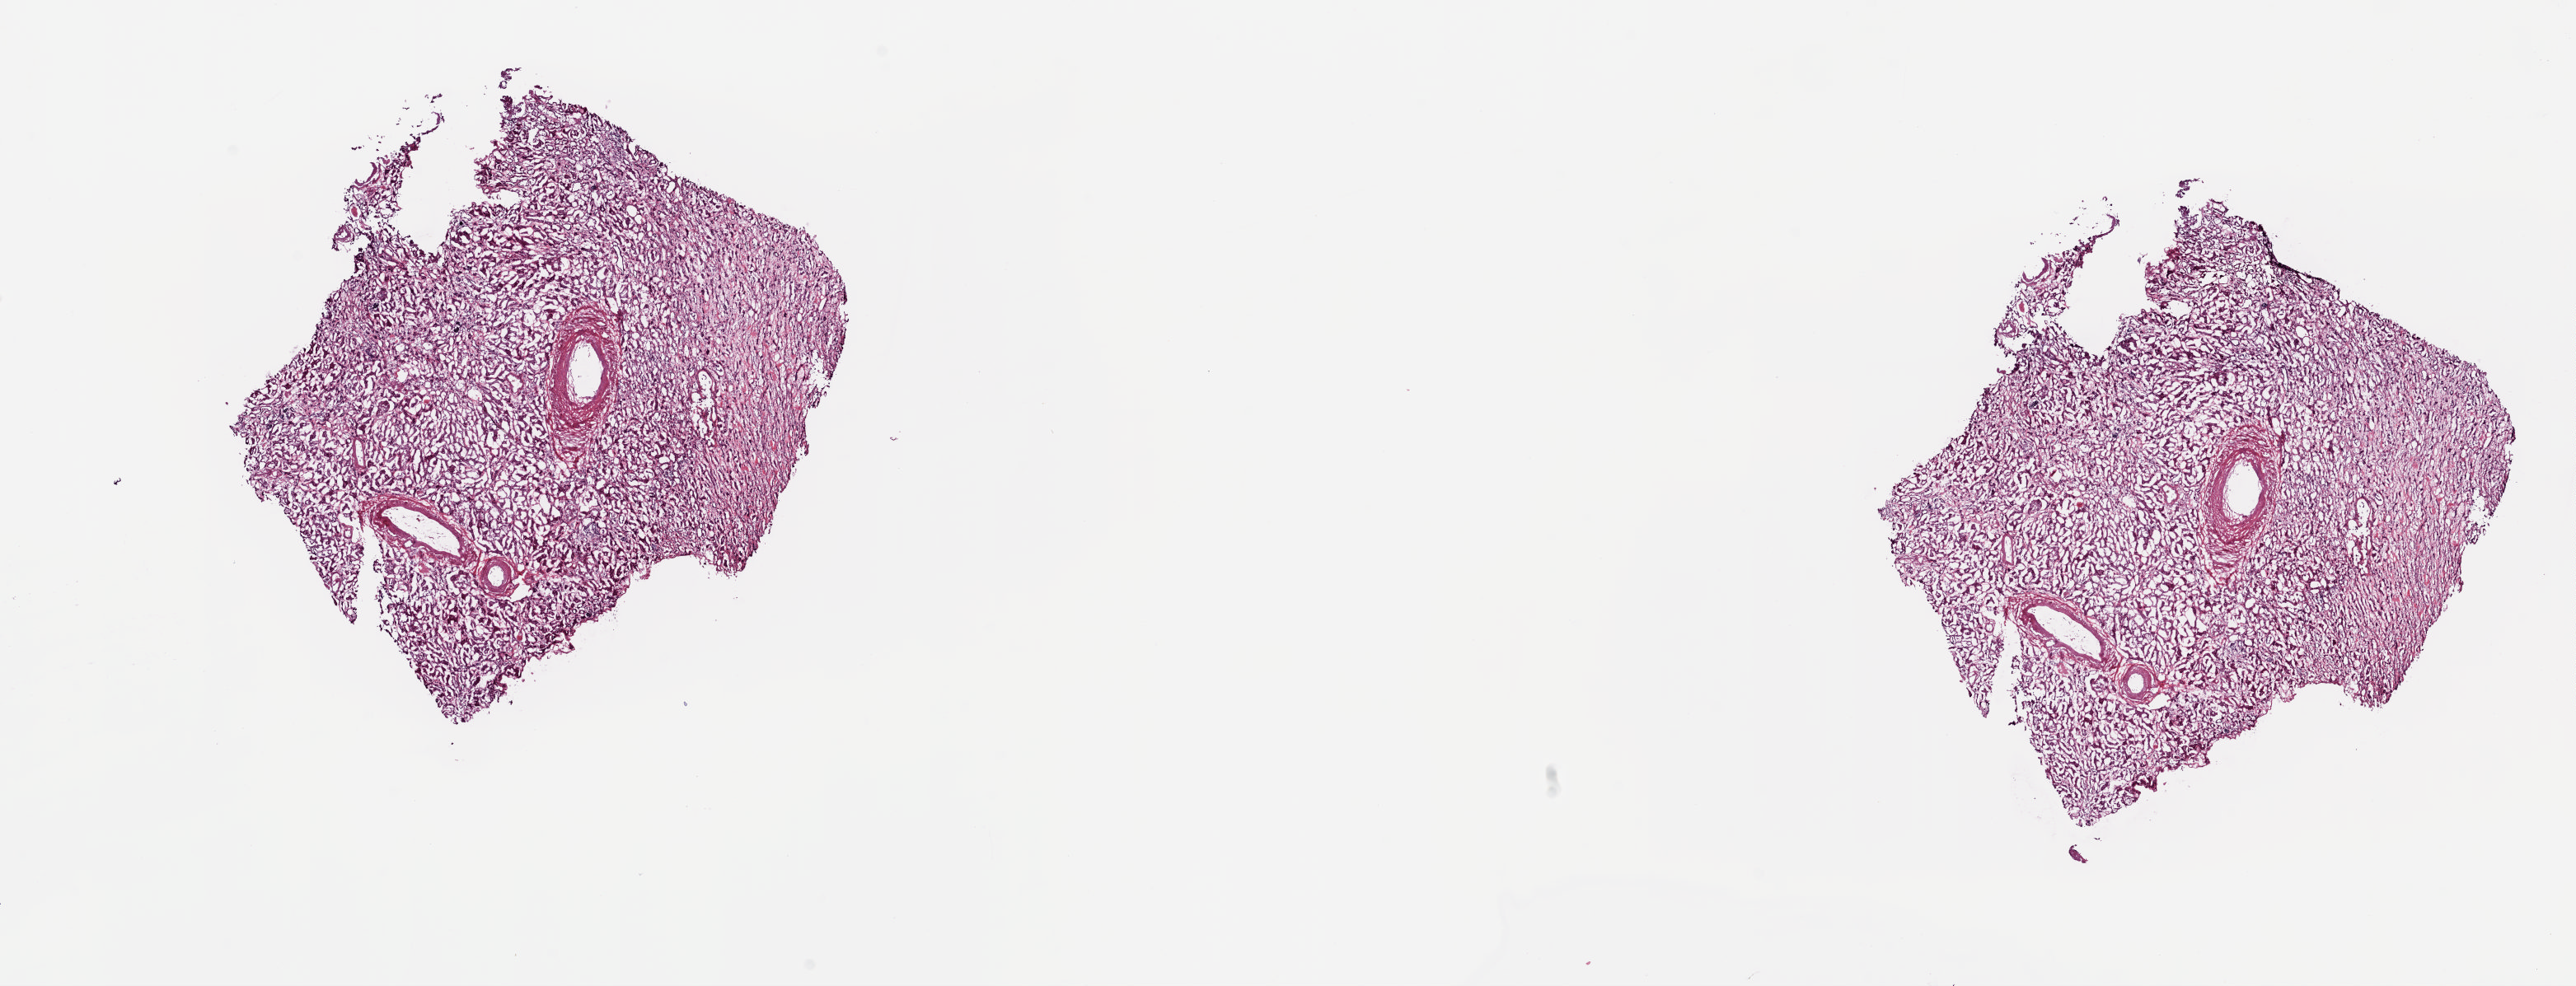
Digitized H&E-stained tissue section (whole slide), shown as a low-resolution overview of the whole scanned area (about 24.8 x 9.5 mm). Frozen section from the top of the tissue portion. Sample: solid tissue normal (non-tumour tissue), kidney. Male patient; age at initial diagnosis 81 years. Pathologist review of this section (percent, as recorded): tumour cells 0%, tumour nuclei 0%, normal cells 100%, stromal cells 0%, necrosis 0%. Infiltration values recorded for this section: lymphocyte infiltration 1%, monocyte infiltration 0%, neutrophil infiltration 0%.
• this section: solid tissue normal sample (biorepository sample class)
• patient diagnosis: Papillary adenocarcinoma, NOS